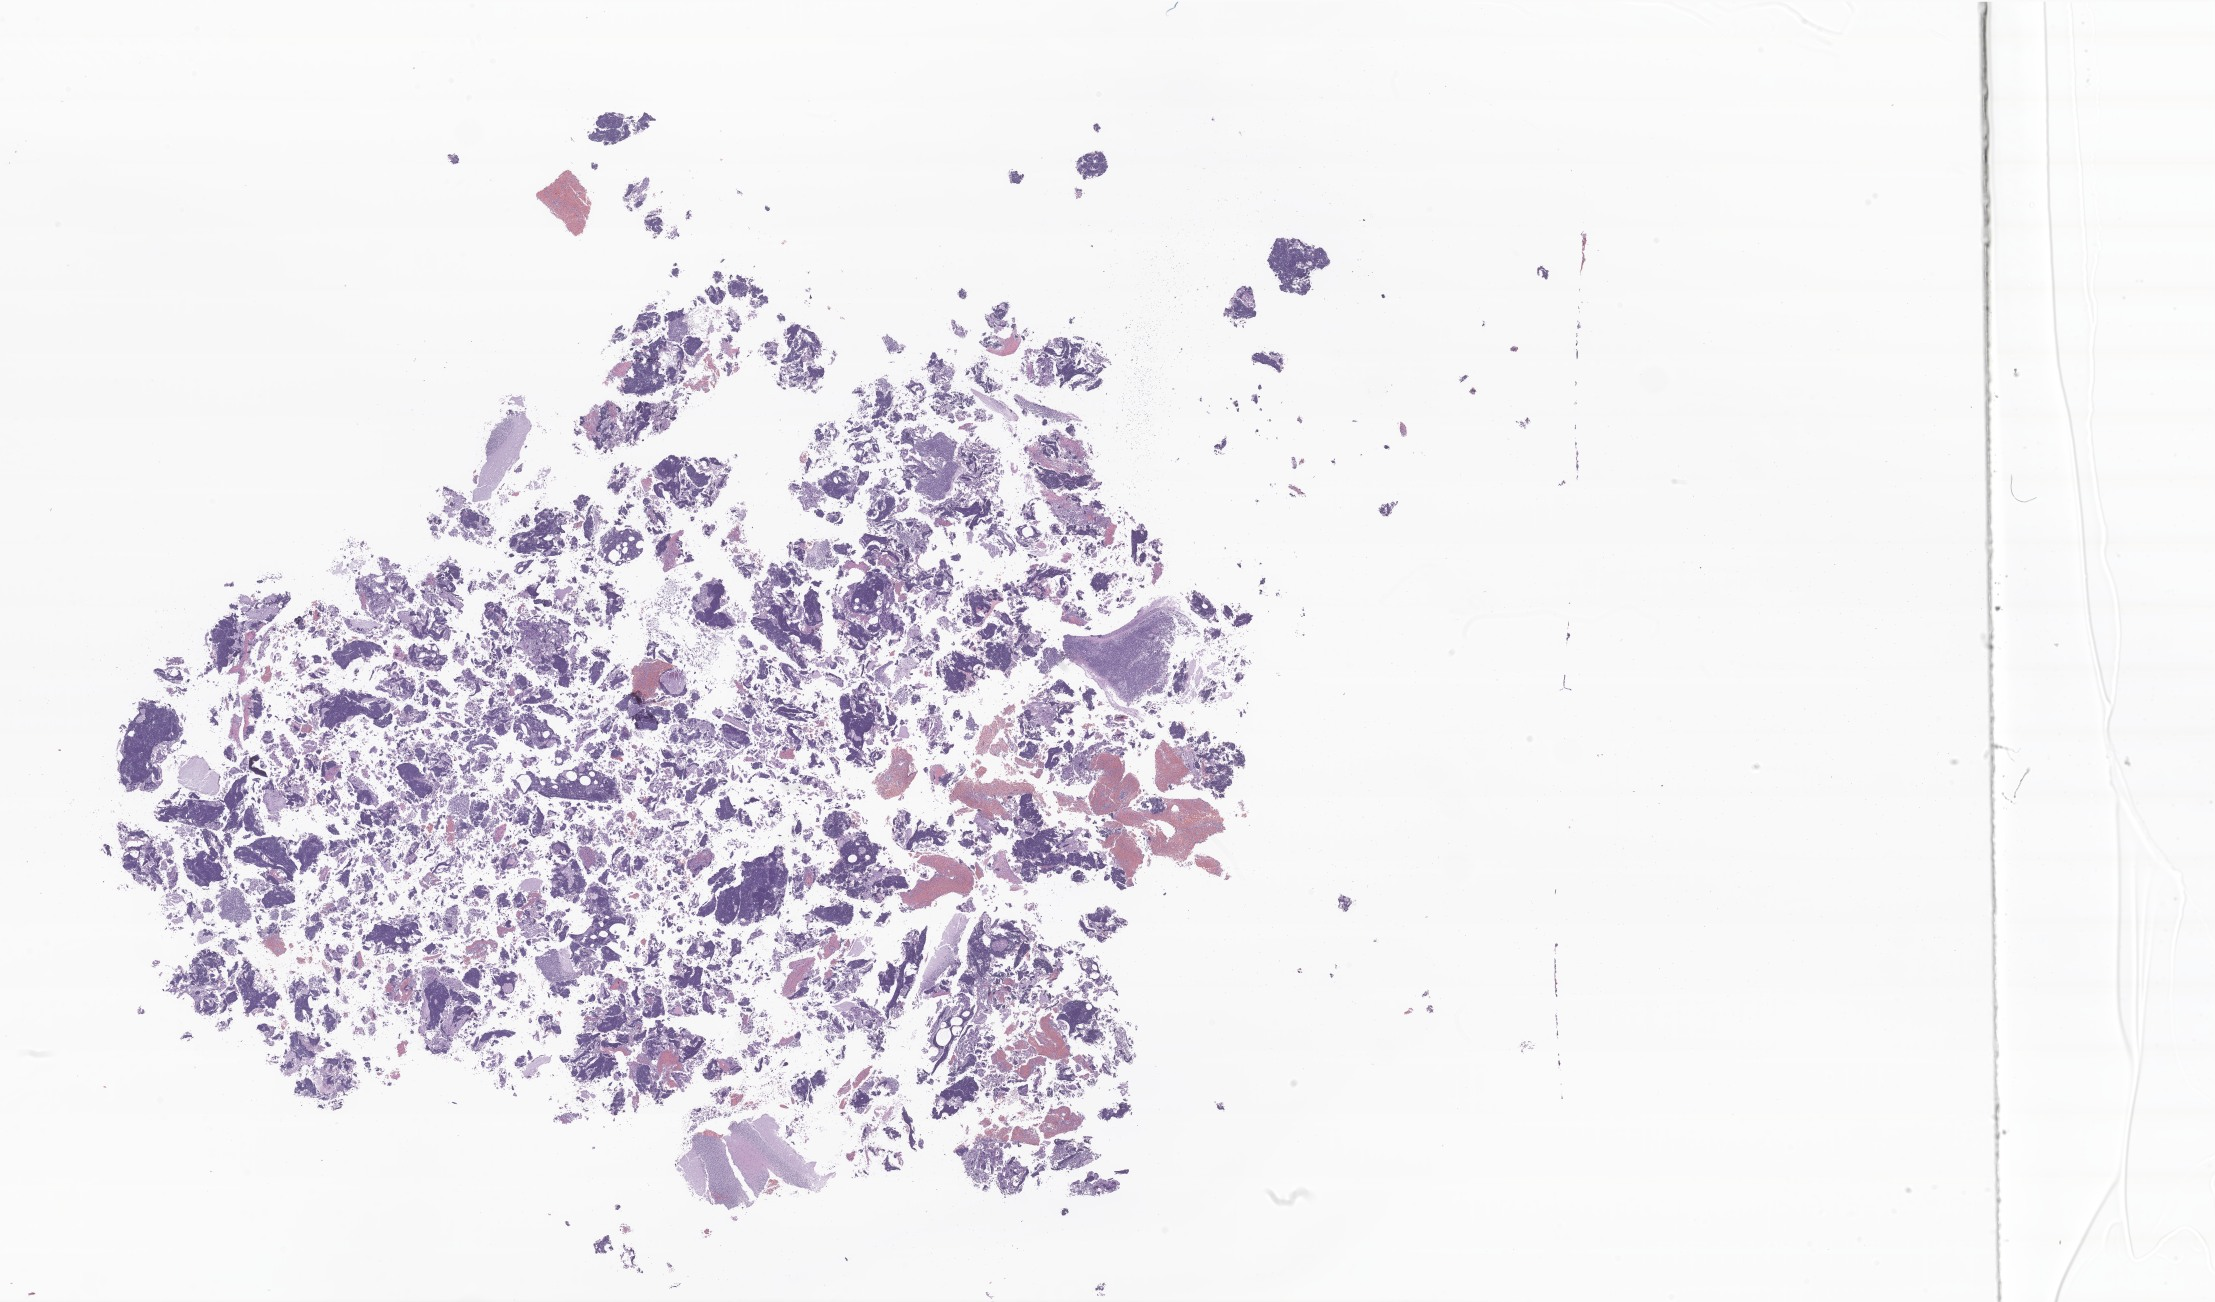
Whole-slide image, haematoxylin and eosin stain of tumor tissue from the brain, whole scanned area (about 37.4 x 22.0 mm) shown as a low-resolution overview, formalin-fixed, paraffin-embedded (FFPE) tissue. Patient female; age 68 months (5 years 8 months).
* recorded diagnosis: Ependymoma, NOS